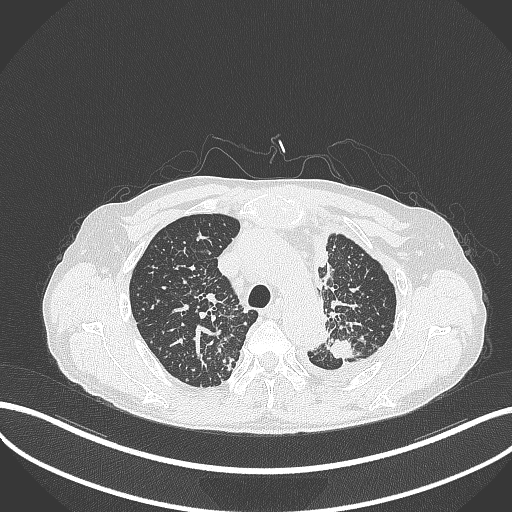
Chest CT, one axial slice; position 267 of 325 along the scan axis; reconstruction kernel B70f; 120 kVp; lung window (W 1500 / L -600 HU); 1 mm slice thickness; 512 × 512 image matrix, field of view 400 × 400 mm. Patient: male, 58 years. Case-level facts recorded for this patient, not image findings: clinical TNM (as recorded): T1c N3 M1.
Structures marked on this image (rectangle marked by the reading radiologist):
- lung tumour (recorded histology: adenocarcinoma): box from (x=327, y=335) to (x=363, y=364) px